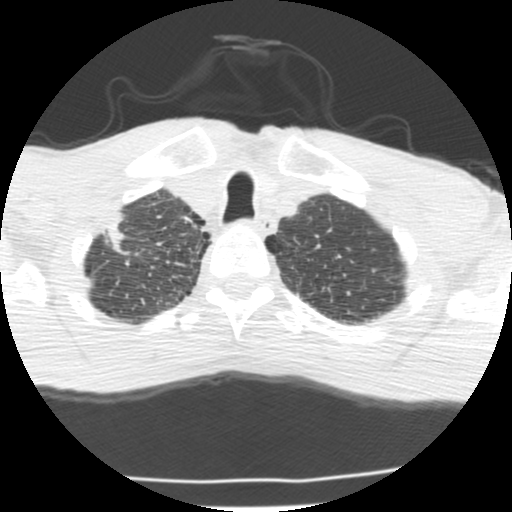
Low-dose screening chest CT, one axial slice; position 187 of 214 along the scan axis; lung window (W 1500 / L -600 HU); 2.5 mm slice thickness; 512 × 512 image matrix.
Outlined on this slice (manually delineated by an expert):
- lesion 1 (tumor, upper lobe of right lung): bounding box (x1, y1, x2, y2) in pixels: (103, 212, 129, 255)